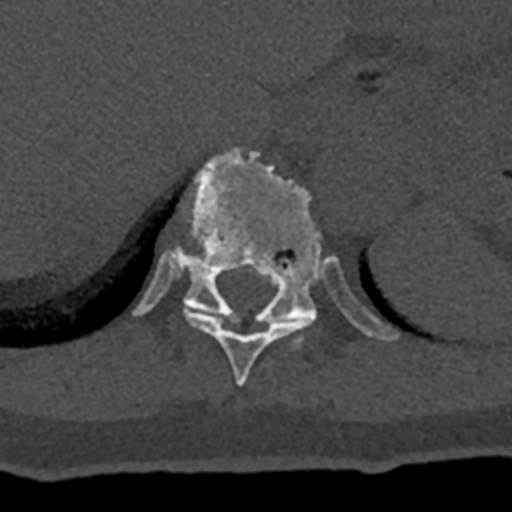
CT including the spine, one axial slice; position 576 of 797 along the scan axis; reconstruction kernel Br40s/3; bone window (W 1800 / L 400 HU); 0.5 mm slice thickness; 512 × 512 image matrix. Male patient, age 74 years. Case-level facts recorded for this patient, not image findings: primary cancer: renal; vertebrae with lytic lesions (as recorded): T10, L1, L2, L3, L4, L5.
Outlined on this slice (semi-automatically segmented with operator editing):
- T10 vertebra: bounding box <184,307,312,387> (left, top, right, bottom; pixels)
- T11 vertebra: <133,148,399,348>